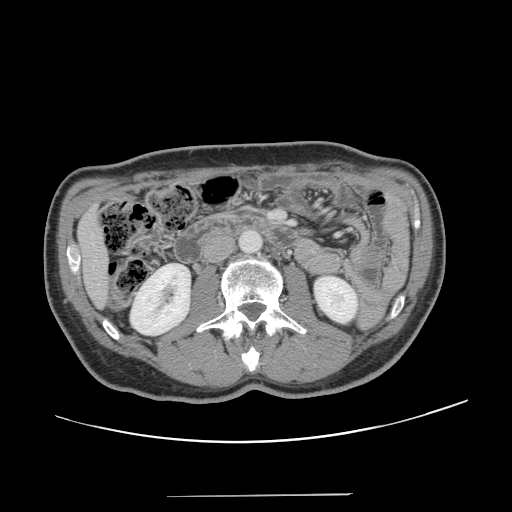
Contrast-enhanced abdominal CT, one axial slice; slice 47 of 131 in the series (ordered by position); intravenous contrast given; soft-tissue window (W 400 / L 40 HU); 2.5 mm slice thickness; 512 × 512 image matrix, field of view 403 × 403 mm. Male patient, age 60 years. Case-level facts recorded for this patient, not image findings: diagnosis: colorectal cancer liver metastases, imaged before liver resection.
Structures marked on this image (outlined manually by an expert reader):
- liver: box from (x=80, y=212) to (x=107, y=306) px
- planned liver remnant (the part of the liver to remain after resection): (x=80, y=212)–(x=107, y=305)